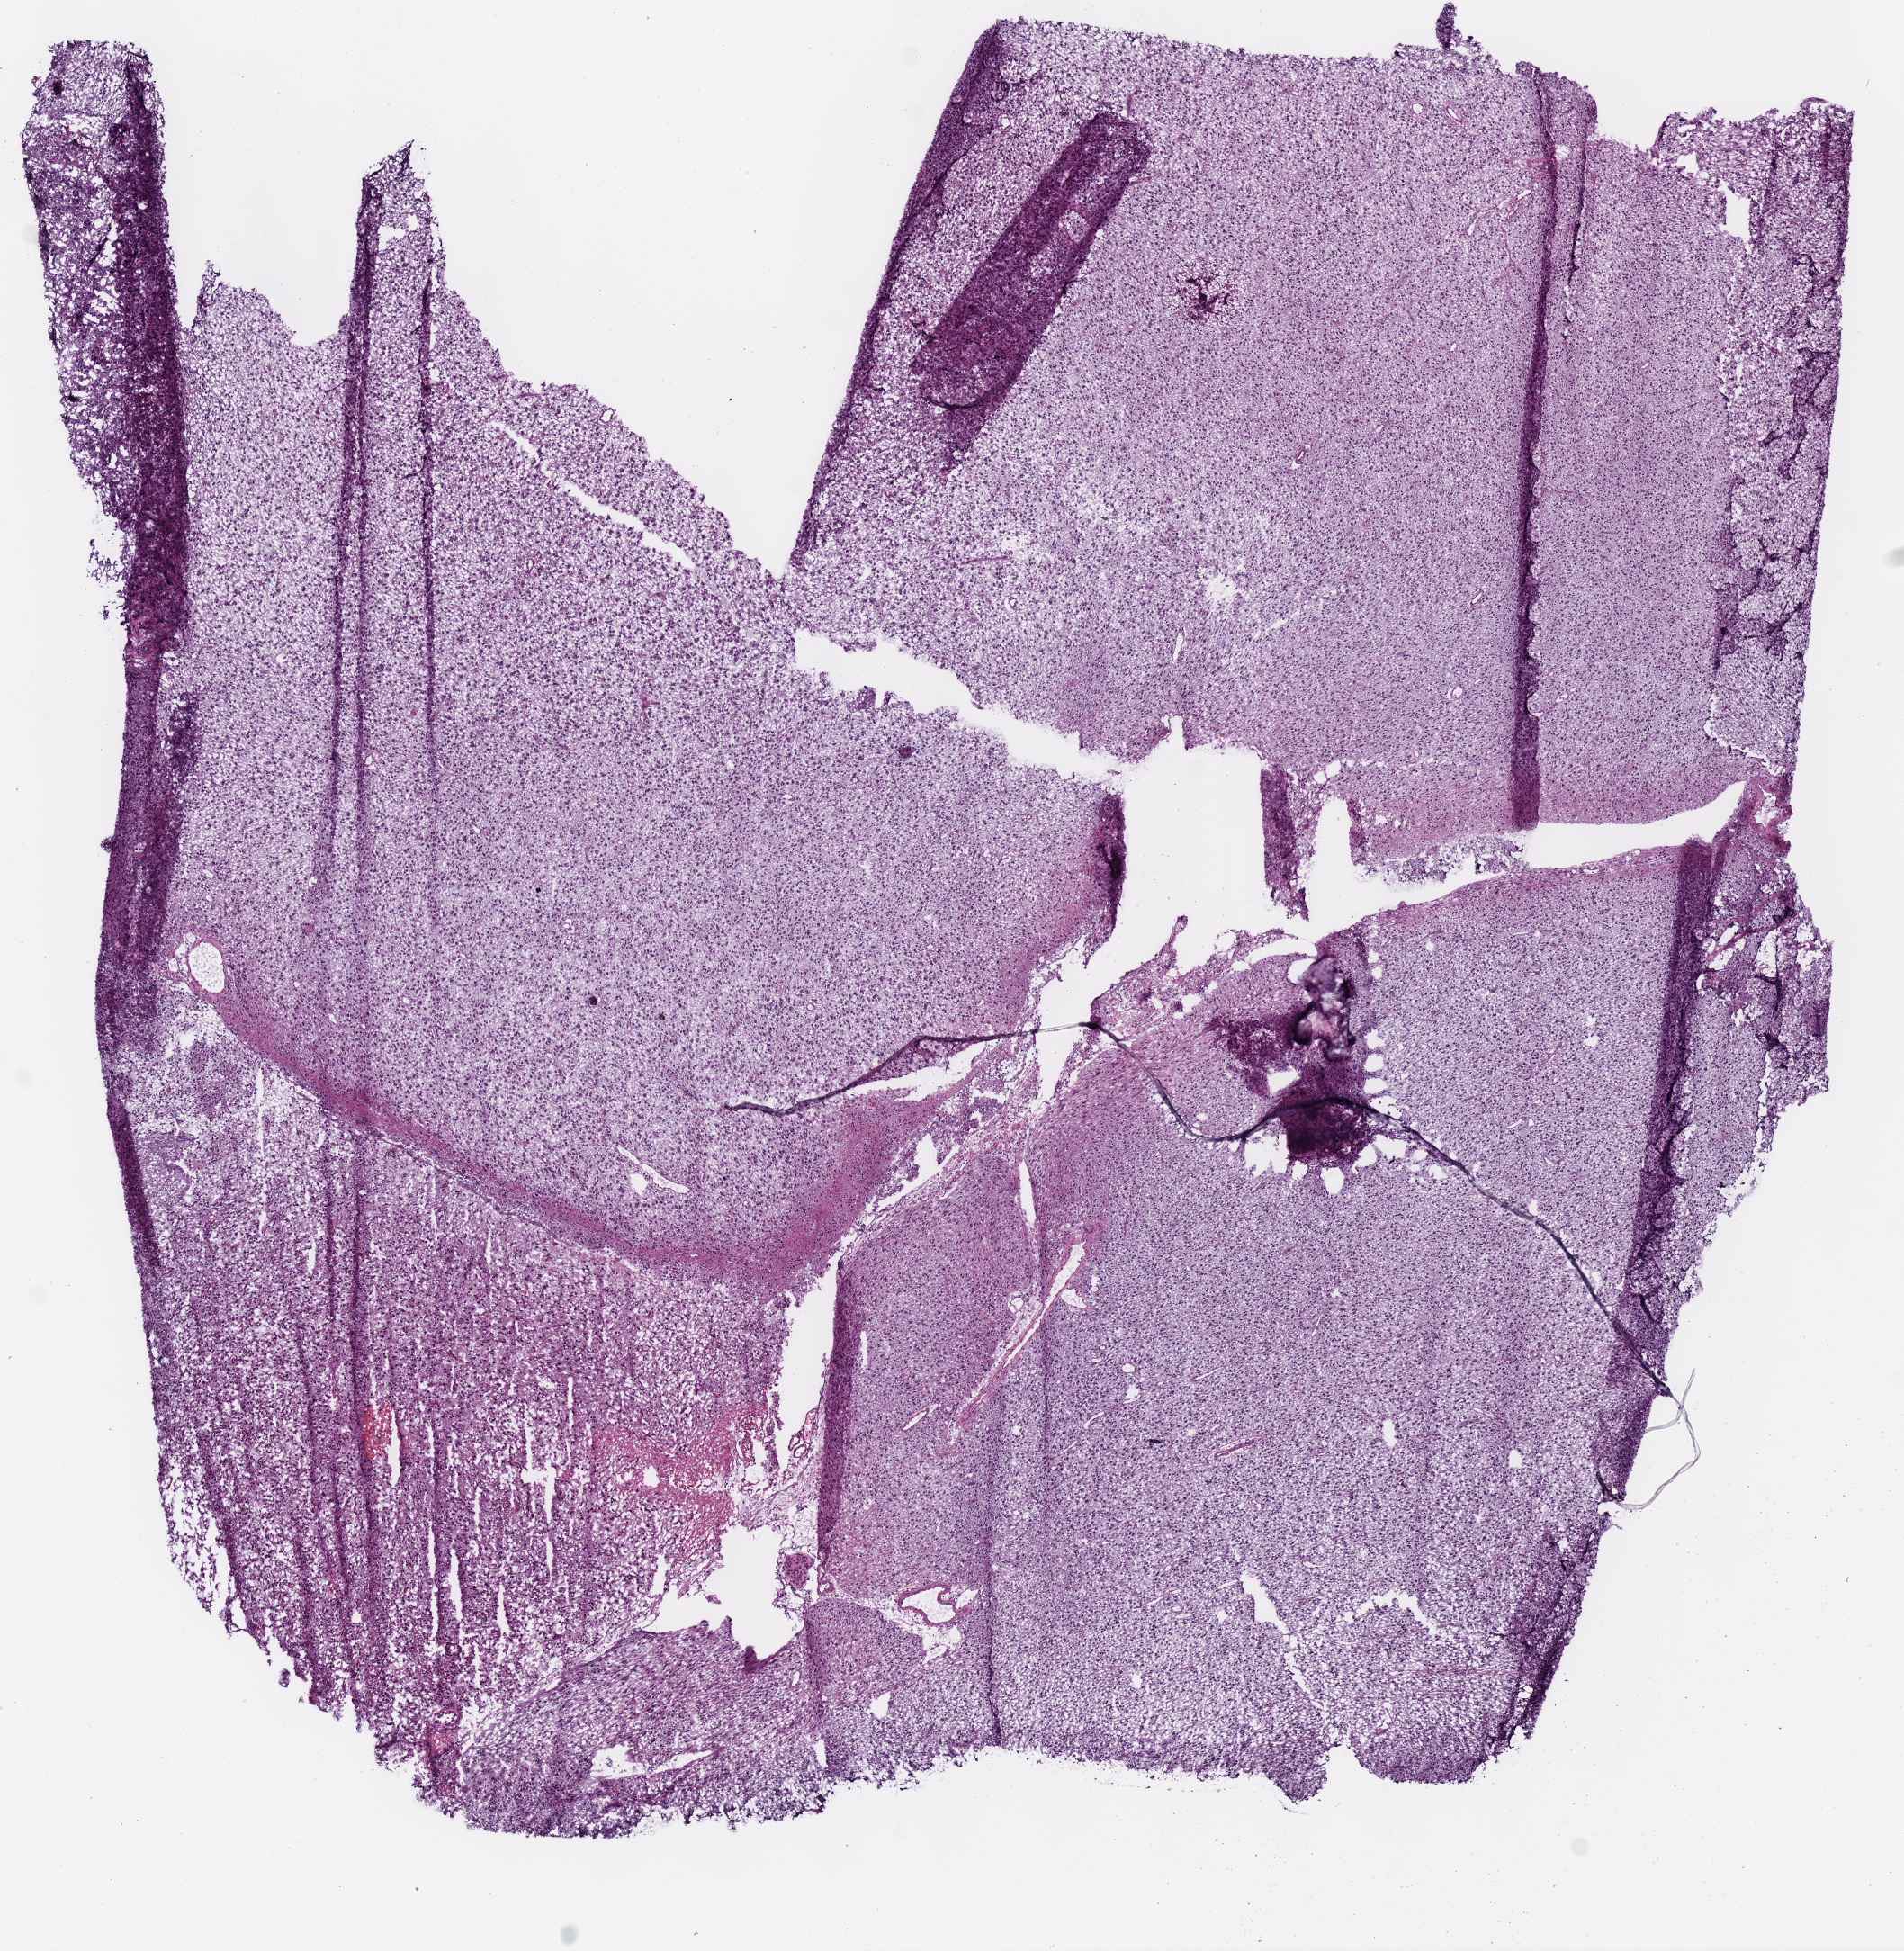
Hematoxylin and eosin (H&E) stained whole-slide image, whole scanned area (about 8.3 x 8.5 mm, from a 40x scan) shown as a low-resolution overview; frozen section from the top of the tissue portion; brain, primary tumour sample. Patient: male, age at initial diagnosis 36 years. Histologic grade: G3 (poorly differentiated). Slide review estimates, as recorded: tumour cells 100%, tumour nuclei 80%, normal cells 0%, stromal cells 0%, necrosis 0%.
- diagnosis: Mixed glioma (cerebrum)